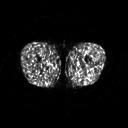
FDG PET of an extremity soft-tissue mass (from a PET/CT study), one axial slice; slice 217 of 267 in the series (ordered by position); 3.27 mm slice thickness; 128 × 128 image matrix, field of view 500 × 500 mm. Patient: male, 27 years. Case-level facts recorded for this patient, not image findings: histological type: extraskeletal osteosarcoma; grade: high; site of the primary tumour: left adductur.
Annotated regions visible in this slice (expert contour drawn on MRI and transferred to this co-registered scan by the dataset authors):
- gross tumour volume (mass): bounding box [x1, y1, x2, y2] px = [71, 62, 89, 70]